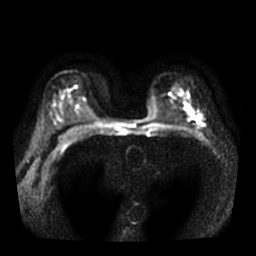
Breast MRI, one axial slice; position 23 of 36 along the scan axis; diffusion-weighted series; image 2 of 4 stored at this slice position (different b-values; order by instance number); 3 T; 5 mm slice thickness; 256 × 256 image matrix. Female patient.
Structures marked on this image (manually delineated by an expert):
- tumour on diffusion-weighted imaging: bounding box (x1, y1, x2, y2) in pixels: (197, 115, 202, 121)